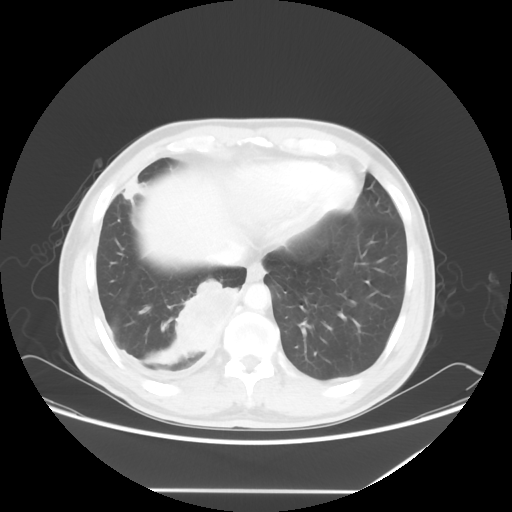
Chest CT, one axial slice. Slice 16 of 60 in the series (ordered by position). Reconstruction kernel STANDARD. 120 kVp. Lung window (W 1500 / L -600 HU). 5 mm slice thickness. 512 × 512 image matrix, field of view 419 × 419 mm. Male patient, age 48 years. Case-level facts recorded for this patient, not image findings: clinical TNM (as recorded): T3 N3 M1a.
Structures marked on this image (rectangle marked by the reading radiologist):
- lung tumour (recorded histology: squamous cell carcinoma): bounding box [x1, y1, x2, y2] px = [165, 278, 243, 356]